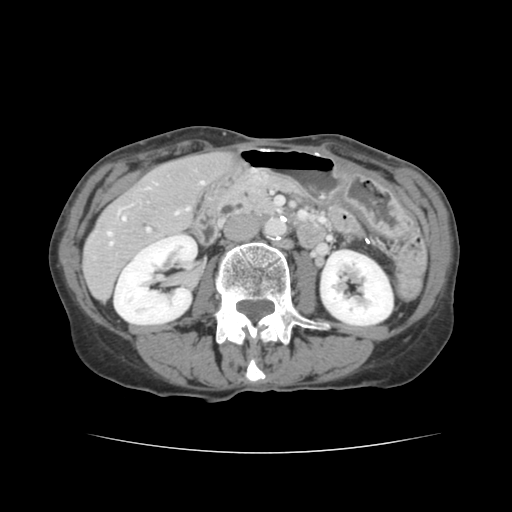
Contrast-enhanced abdominal CT, one axial slice. Position 51 of 136 along the scan axis. Intravenous contrast given. Soft-tissue window (W 400 / L 40 HU). 2.5 mm slice thickness. 512 × 512 image matrix, field of view 319 × 319 mm. Female patient, age 77 years. From the clinical record (not read from this slice): diagnosis: colorectal cancer liver metastases, imaged before liver resection; multiple liver metastases: yes; largest metastasis: 3 cm; chemotherapy before resection: yes.
Annotated regions visible in this slice (expert manual segmentation):
- hepatic veins: bounding box (x1, y1, x2, y2) in pixels: (108, 181, 203, 245)
- liver: (85, 153, 230, 299)
- planned liver remnant (the part of the liver to remain after resection): (168, 153, 230, 194)
- portal vein (with intrahepatic branches): (147, 188, 150, 232)